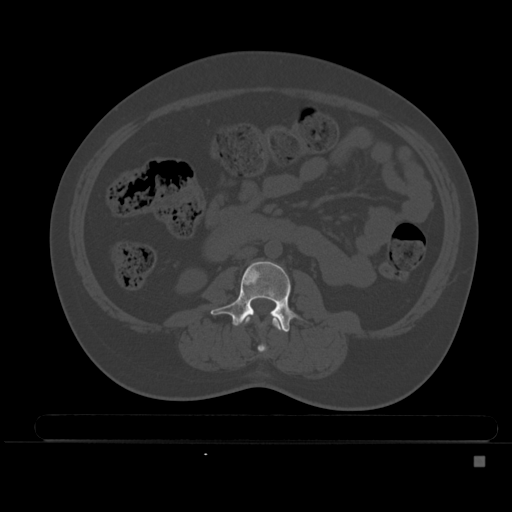
CT including the spine, one axial slice; bone window (W 1800 / L 400 HU); 1.5 mm slice thickness; 512 × 512 image matrix, field of view 404 × 404 mm. Patient: female, 33 years. From the clinical record (not read from this slice): primary cancer: breast; vertebrae with lytic lesions (as recorded): T1.
Annotated regions visible in this slice (semi-automatic segmentation, software-assisted and operator-edited):
- L2 vertebra: box from (x=242, y=315) to (x=283, y=353) px
- L3 vertebra: (x=210, y=261)–(x=297, y=332)